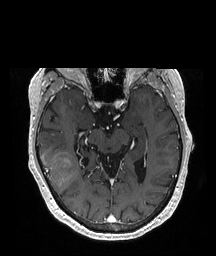
Brain MRI from a brain-tumour surgery series, one axial slice. Position 124 of 208 along the scan axis. T1-weighted post-contrast. 1 mm slice thickness. 216 × 256 image matrix, field of view 216 × 256 mm. Case-level facts recorded for this patient, not image findings: histopathology: Glioblastoma; WHO grade: 4; IDH mutation: no.
Structures marked on this image (expert manual segmentation):
- tumour: box from (x=39, y=152) to (x=78, y=194) px